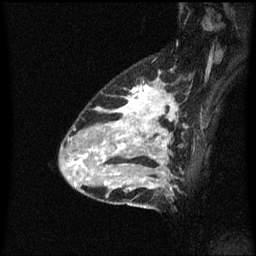
Breast MRI (dynamic contrast-enhanced), one sagittal slice. Position 42 of 60 along the scan axis. Dynamic contrast-enhanced series, image 2 of 3 at this slice position (ordered by acquisition). 1.5 T. TE 4.2 ms, TR 8.4 ms. 256 × 256 image matrix. Patient: female, 34 years. Case-level facts recorded for this patient, not image findings: setting: breast cancer imaged before/during neoadjuvant chemotherapy; receptor status: HR-positive, HER2-negative.
Structures marked on this image (semi-automatically segmented with operator editing):
- analysis volume of interest (the breast-tissue region the enhancement analysis was run in; not a lesion): bounding box [x1, y1, x2, y2] px = [69, 80, 178, 209]
- tumour enhancement mask (voxels above the 70 % enhancement threshold inside the analysis volume of interest): [70, 86, 174, 189]